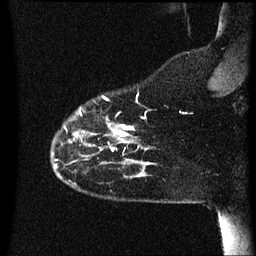
Breast MRI (dynamic contrast-enhanced), one sagittal slice. Slice 10 of 60 in the series (ordered by position). Dynamic contrast-enhanced series, image 2 of 3 at this slice position (ordered by acquisition). 1.5 T. TE 4.2 ms, TR 8.4 ms. 2.2 mm slice thickness. 256 × 256 image matrix, field of view 200 × 200 mm. Female patient, age 35 years. Case-level facts recorded for this patient, not image findings: setting: breast cancer imaged before/during neoadjuvant chemotherapy; receptor status: HER2-positive.
Structures marked on this image (semi-automatically segmented with operator editing):
- analysis volume of interest (the breast-tissue region the enhancement analysis was run in; not a lesion): box from (x=52, y=94) to (x=157, y=173) px
- tumour enhancement mask (voxels above the 70 % enhancement threshold inside the analysis volume of interest): (x=75, y=110)–(x=145, y=151)